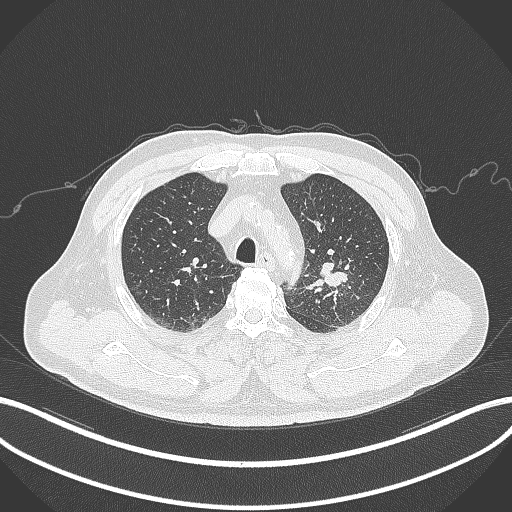
Chest CT, one axial slice. Position 236 of 286 along the scan axis. 120 kVp. Lung window (W 1500 / L -600 HU). 512 × 512 image matrix, field of view 400 × 400 mm. Male patient, age 67 years. From the clinical record (not read from this slice): clinical TNM (as recorded): T2a N1 M0.
Annotated regions visible in this slice (rectangle marked by the reading radiologist):
- lung tumour (recorded histology: adenocarcinoma): box from (x=318, y=257) to (x=351, y=289) px